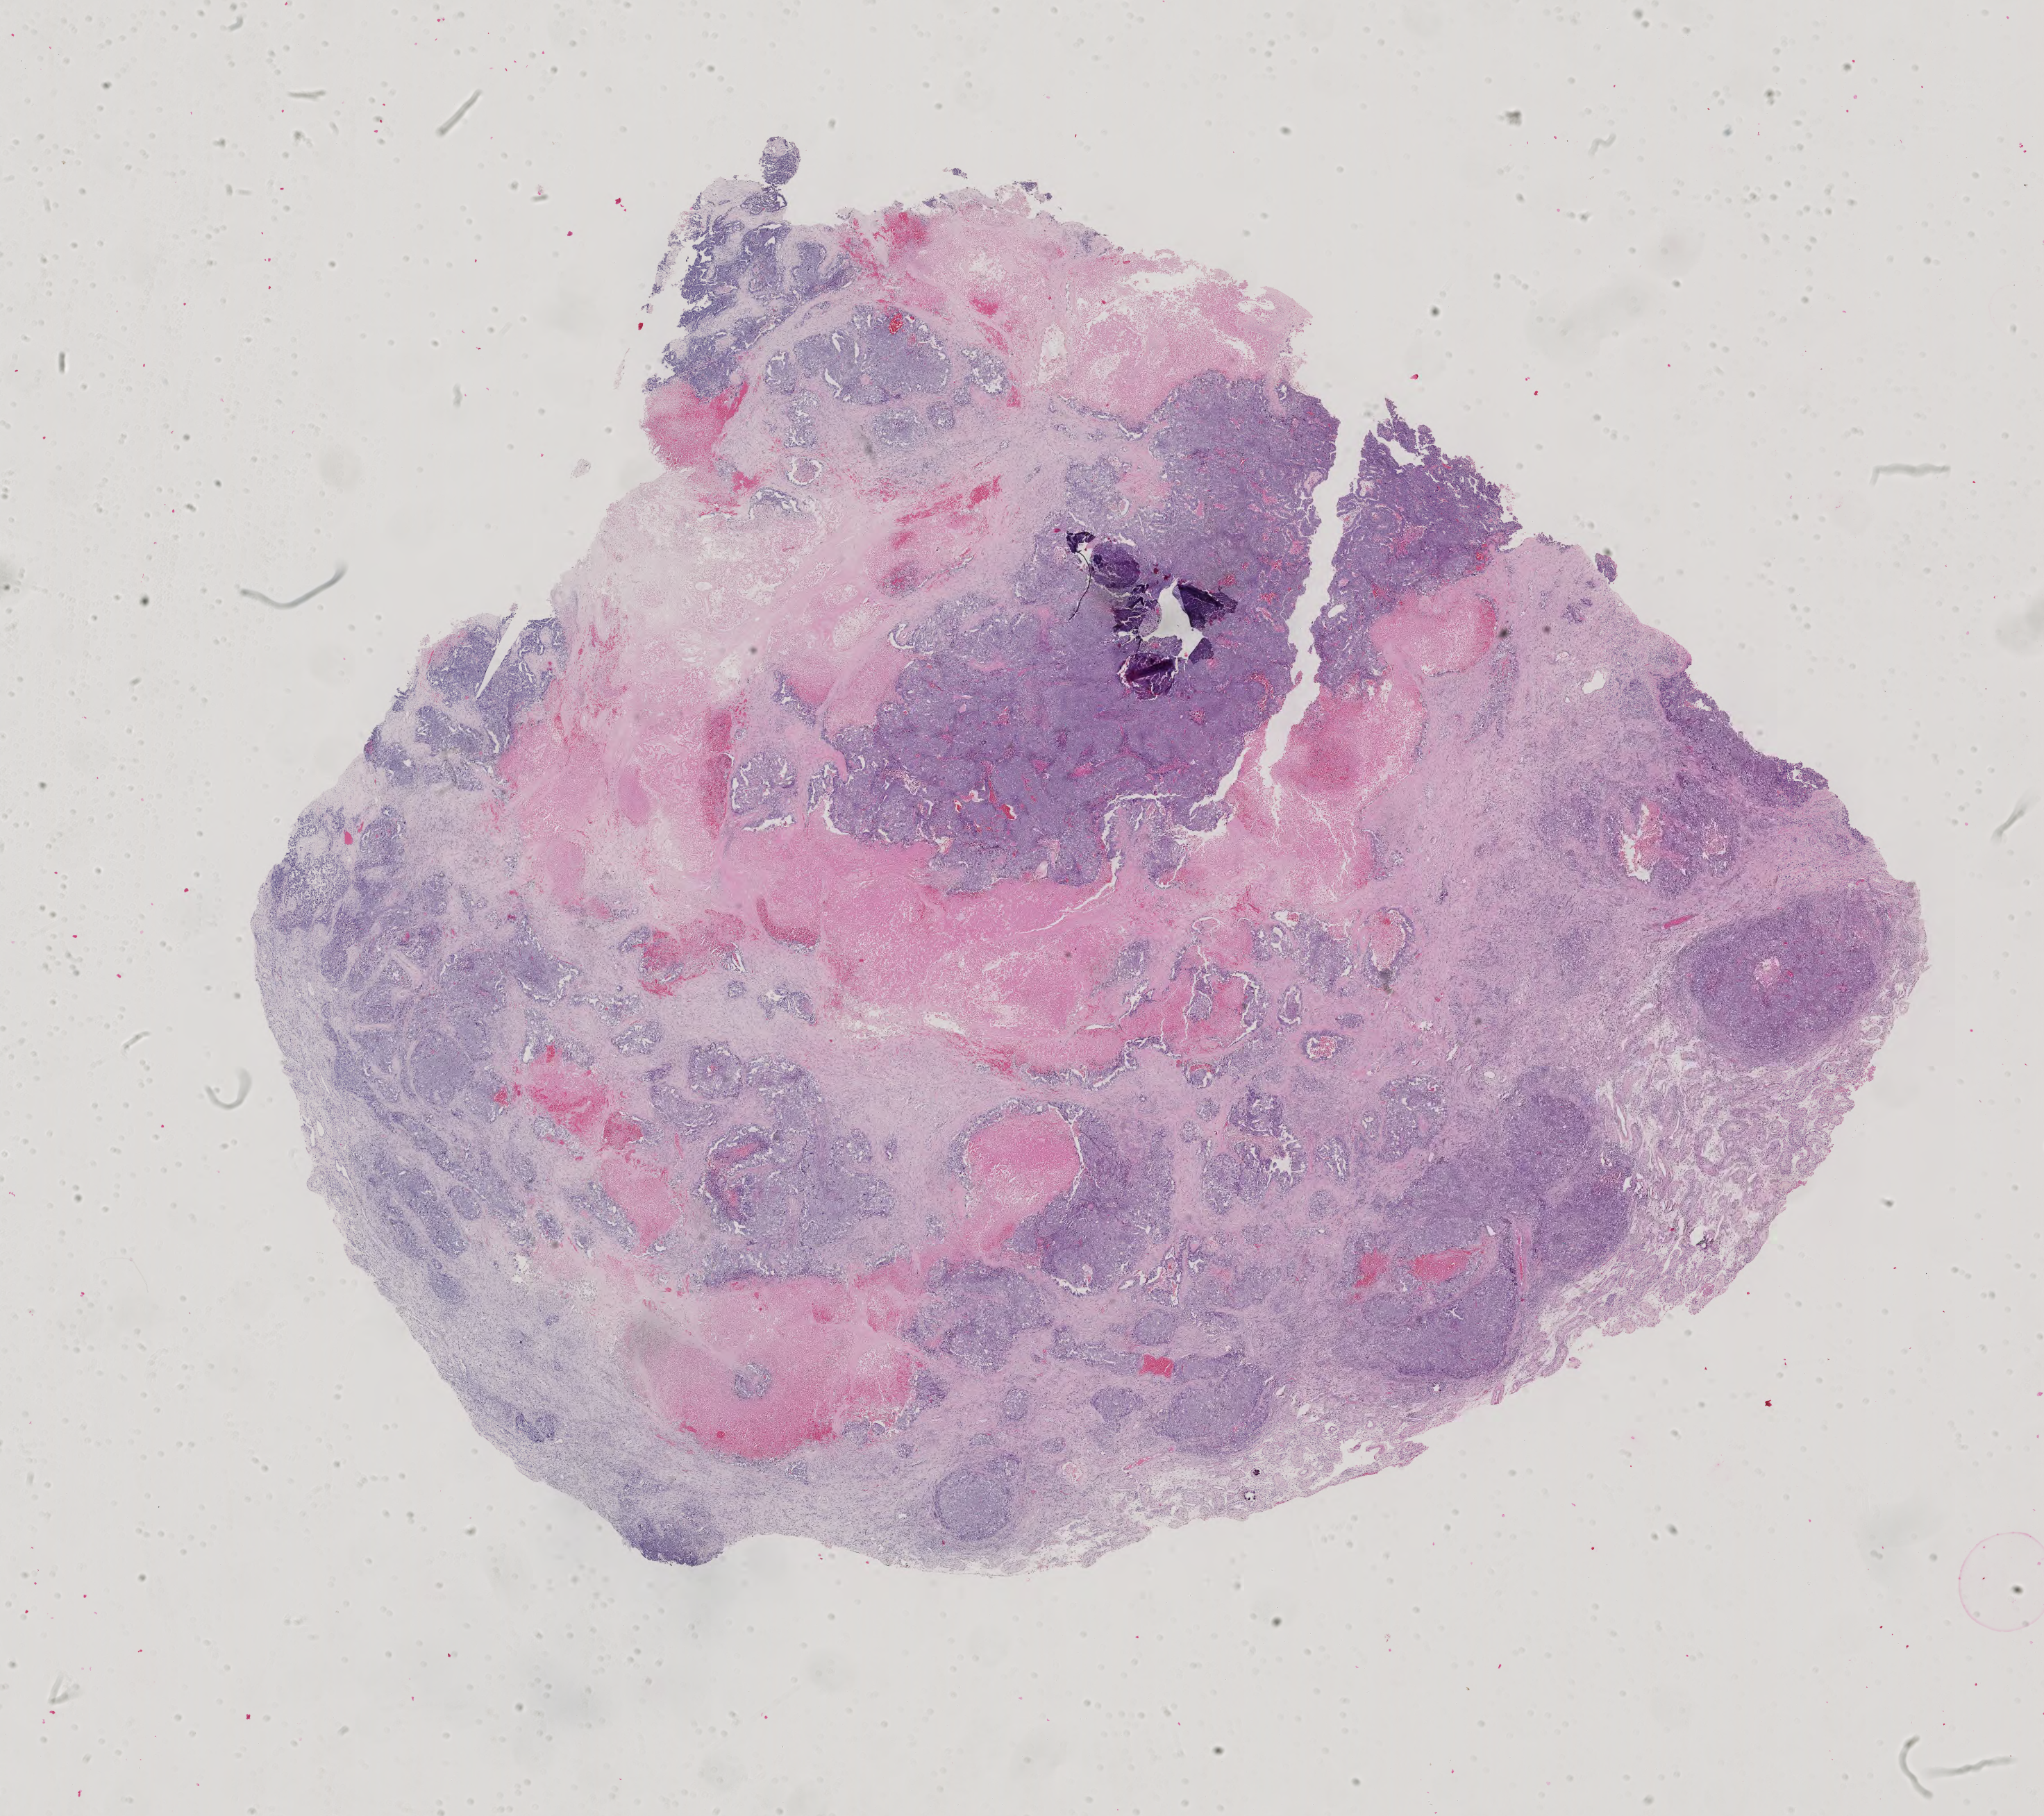
Digitized H&E tissue section (whole slide) — whole scanned area (about 21.5 x 19.1 mm) shown as a low-resolution overview, FFPE section, primary tumour sample from the testis. Male, age 21 years at initial diagnosis.
* laterality: right
* AJCC pathologic stage: IB
* TNM: T2 N0 M0
* diagnosis: Embryonal carcinoma, NOS